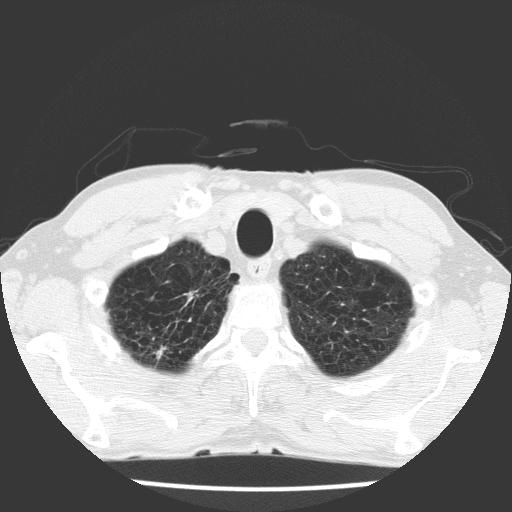
Axial slice from a low-dose chest CT screening exam, first (baseline) screen, lung window (W 1500 / L -600 HU), 2 mm slice thickness, lung (sharp) reconstruction kernel (FC51), slice 15 of 172 in the series, 512 × 512 image matrix. Male, age 63 years at enrolment. Current smoker at enrolment.
Expert reader's lesion annotation, bounding box <163,280,217,333> (left, top, right, bottom; pixels). No non-calcified nodule or mass ≥4 mm was recorded by the screening reader at this exam. Lung cancer was diagnosed 741 days after this screen (after the third annual screen): adenocarcinoma, NOS, right upper lobe, moderately differentiated (G2), stage IIIB (AJCC 6th edition), 17 mm at pathology.